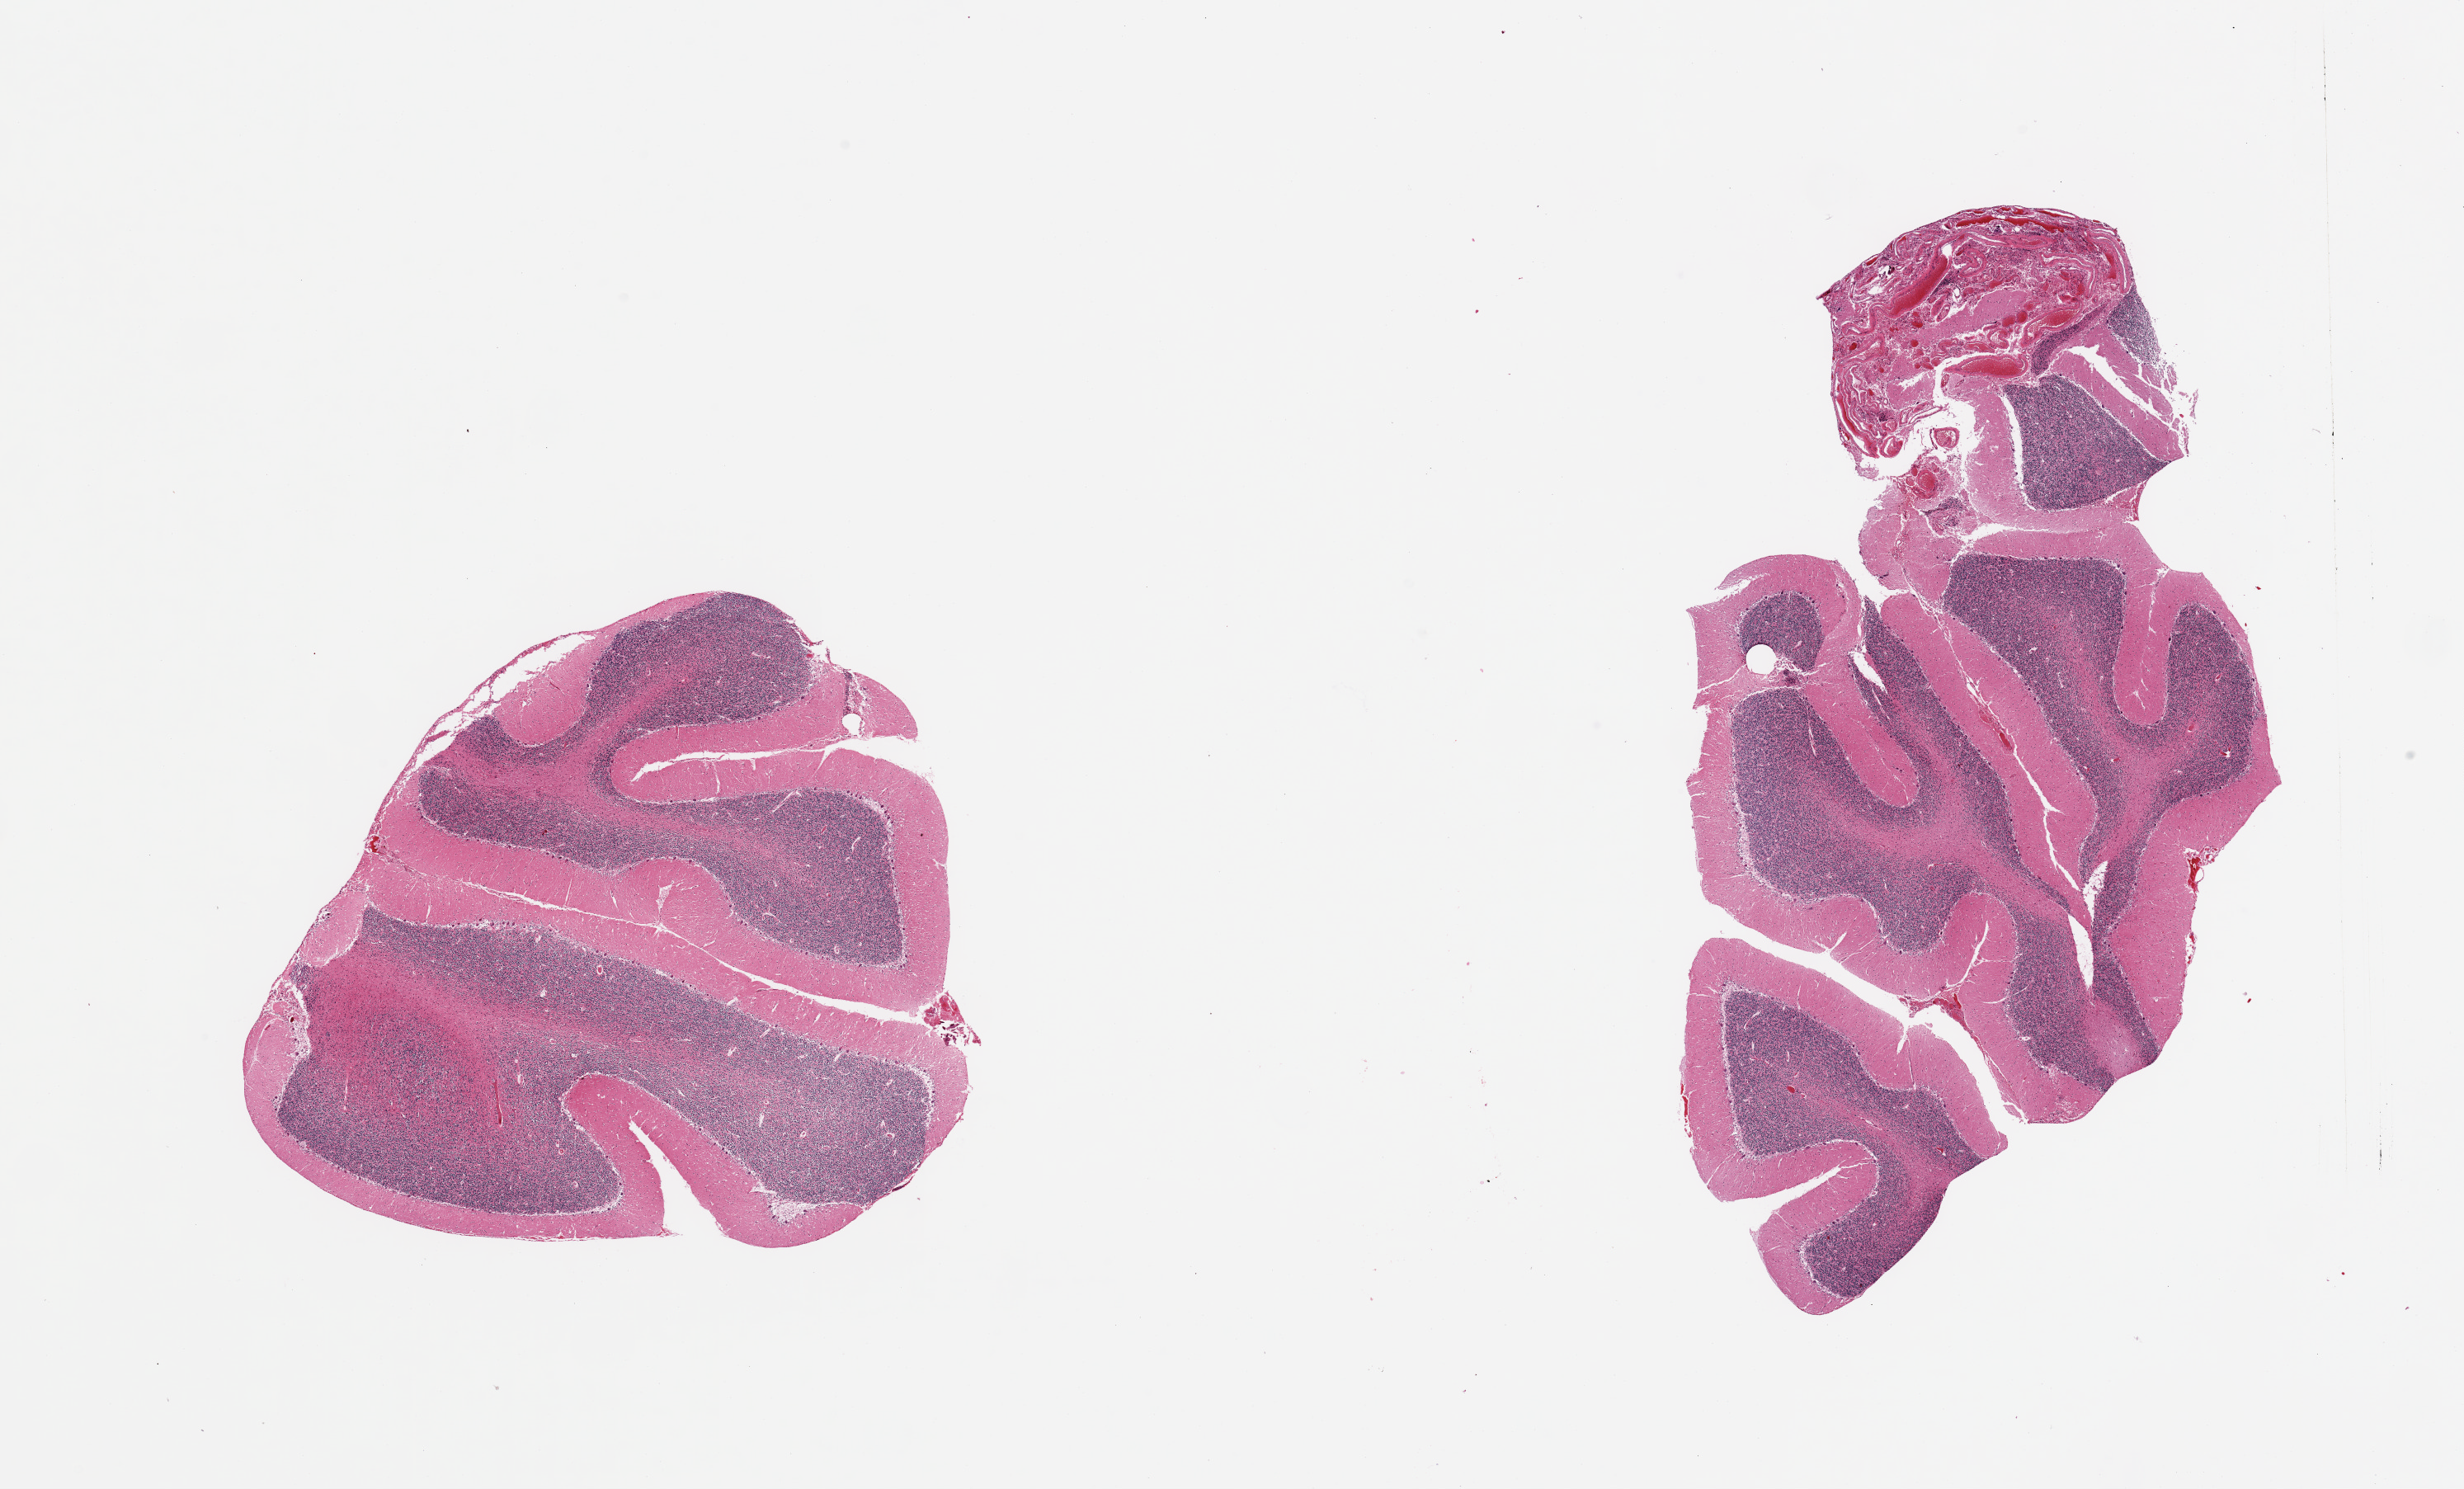
Whole-slide image, H&E stain, brightfield, low-resolution overview of the scanned area, about 23.6 x 14.3 mm, PAXgene-fixed paraffin-embedded (PFPE) section, section of cerebellum (target tissue), tissue donor sample. Donor: female.
Reviewer comment on this tissue sample: 2 pieces, no abnormalities.